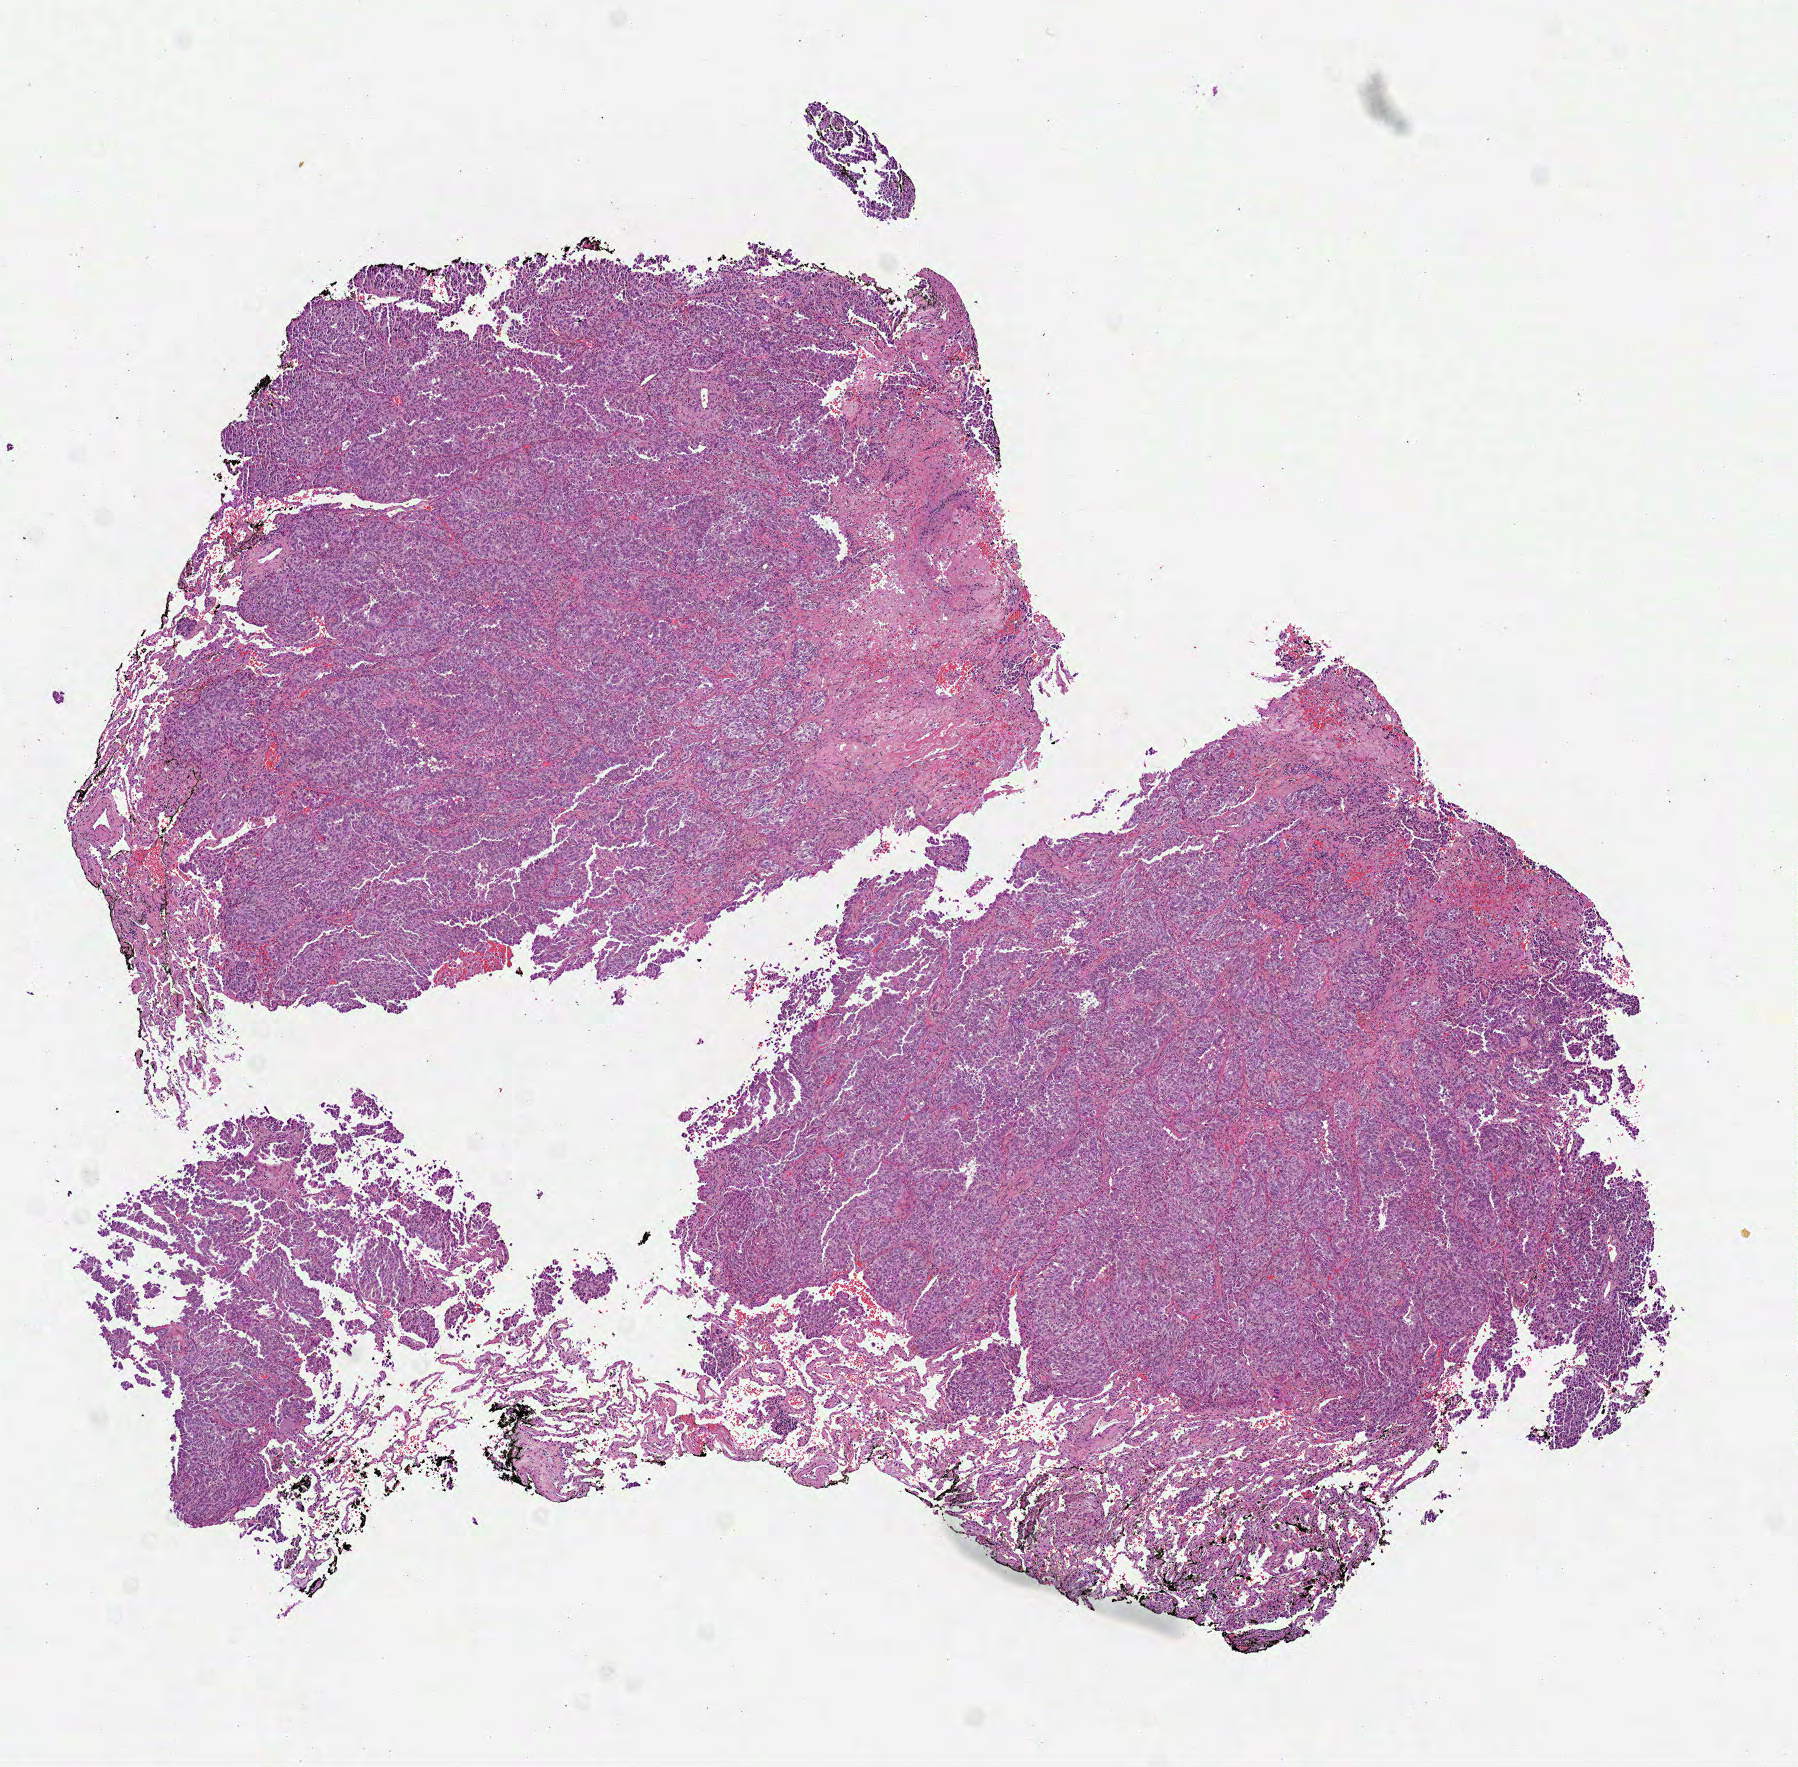
Whole-slide histology image, H&E, low-resolution overview of the scanned area, about 7.3 x 7.1 mm. Formalin-fixed paraffin-embedded (FFPE) diagnostic section. Lung, primary tumour sample. Male, age 64 years at initial diagnosis.
TNM: T1b N0 MX. AJCC pathologic stage: IA. Histologic diagnosis: Adenocarcinoma, NOS (lower lobe, lung).